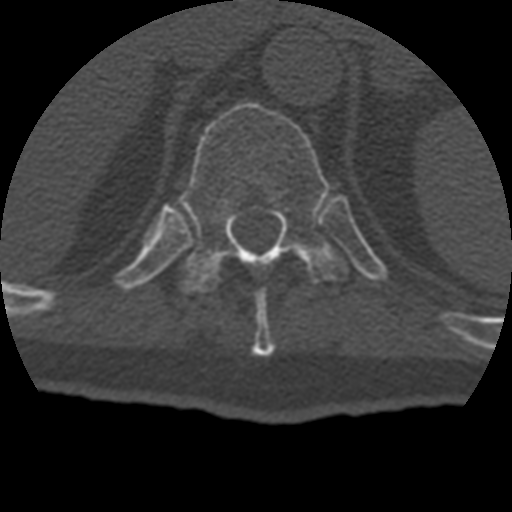
CT including the spine, one axial slice; position 203 of 399 along the scan axis; bone window (W 1800 / L 400 HU); 1.25 mm slice thickness; 512 × 512 image matrix, field of view 160 × 160 mm. Patient age 69 years. From the clinical record (not read from this slice): primary cancer: prostate.
Structures marked on this image (semi-automatically segmented with operator editing):
- T10 vertebra: box from (x=253, y=291) to (x=275, y=356) px
- T11 vertebra: (x=178, y=102)–(x=349, y=292)